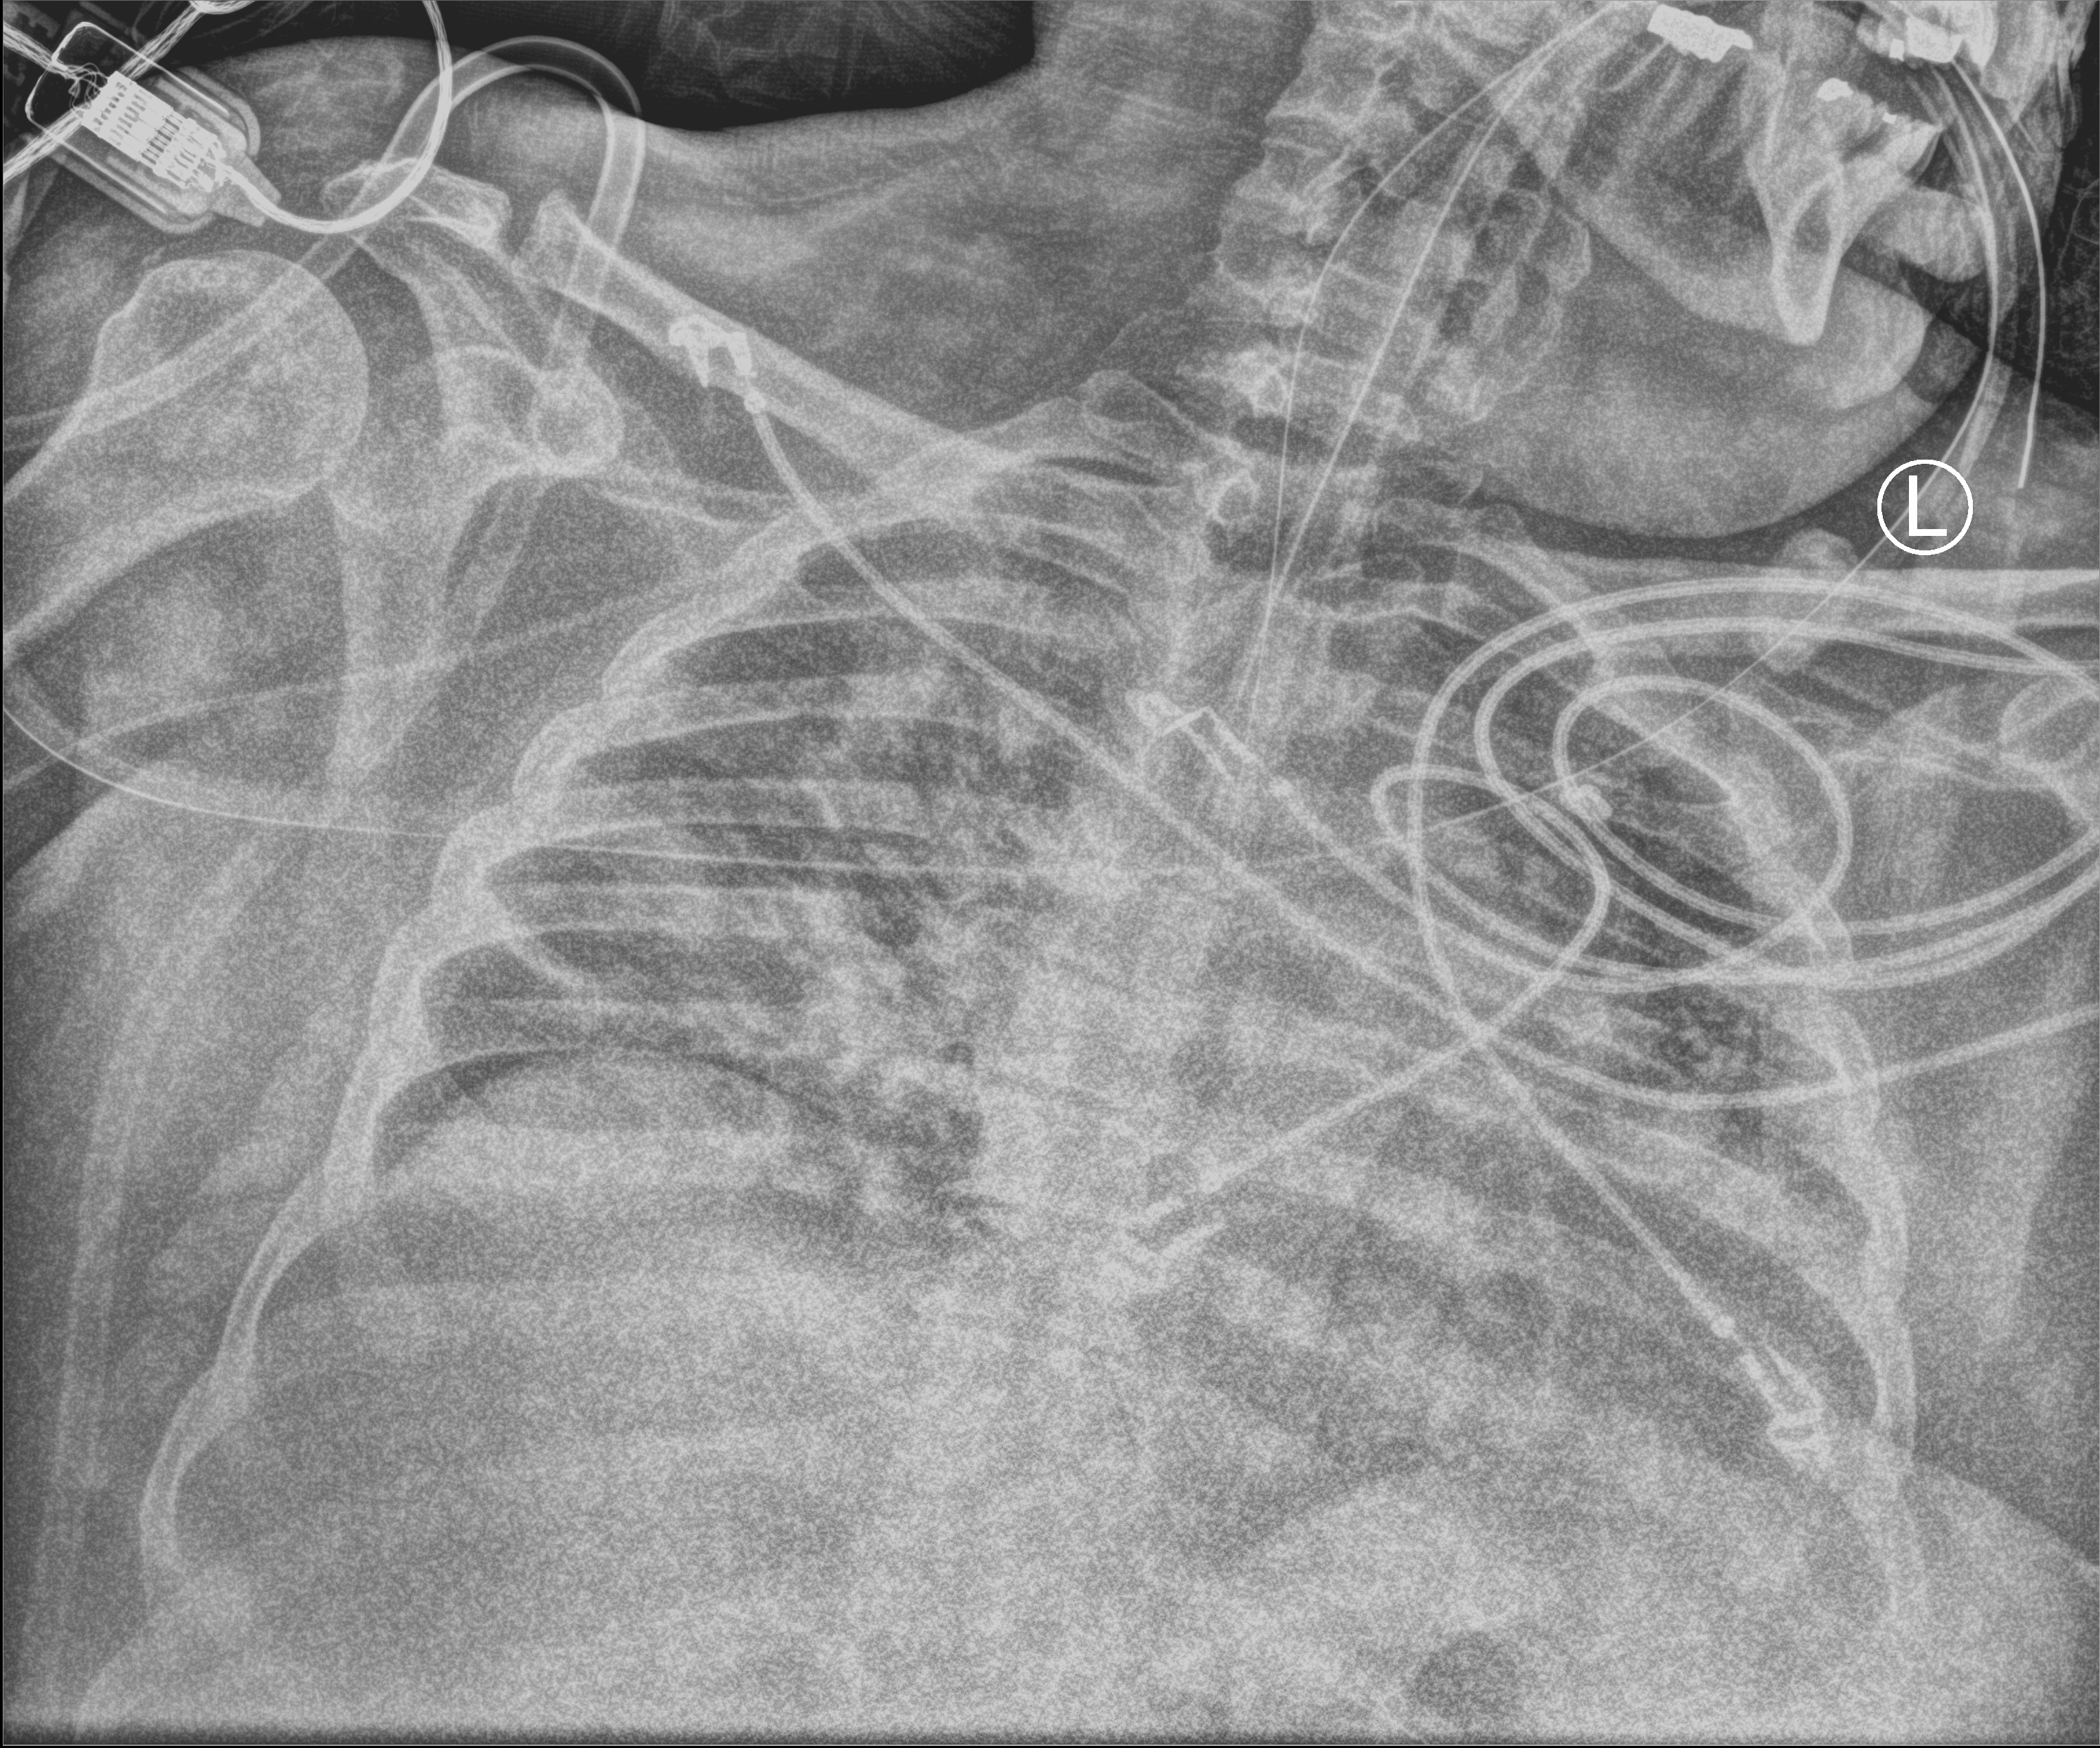
Chest X-ray (portable), anteroposterior (AP) projection. Patient hospitalised with COVID-19; male, aged 18–59 years.
Admission-level facts for this patient (not findings on this image; timing relative to this image not recorded): admitted to intensive care during this hospital stay: yes.